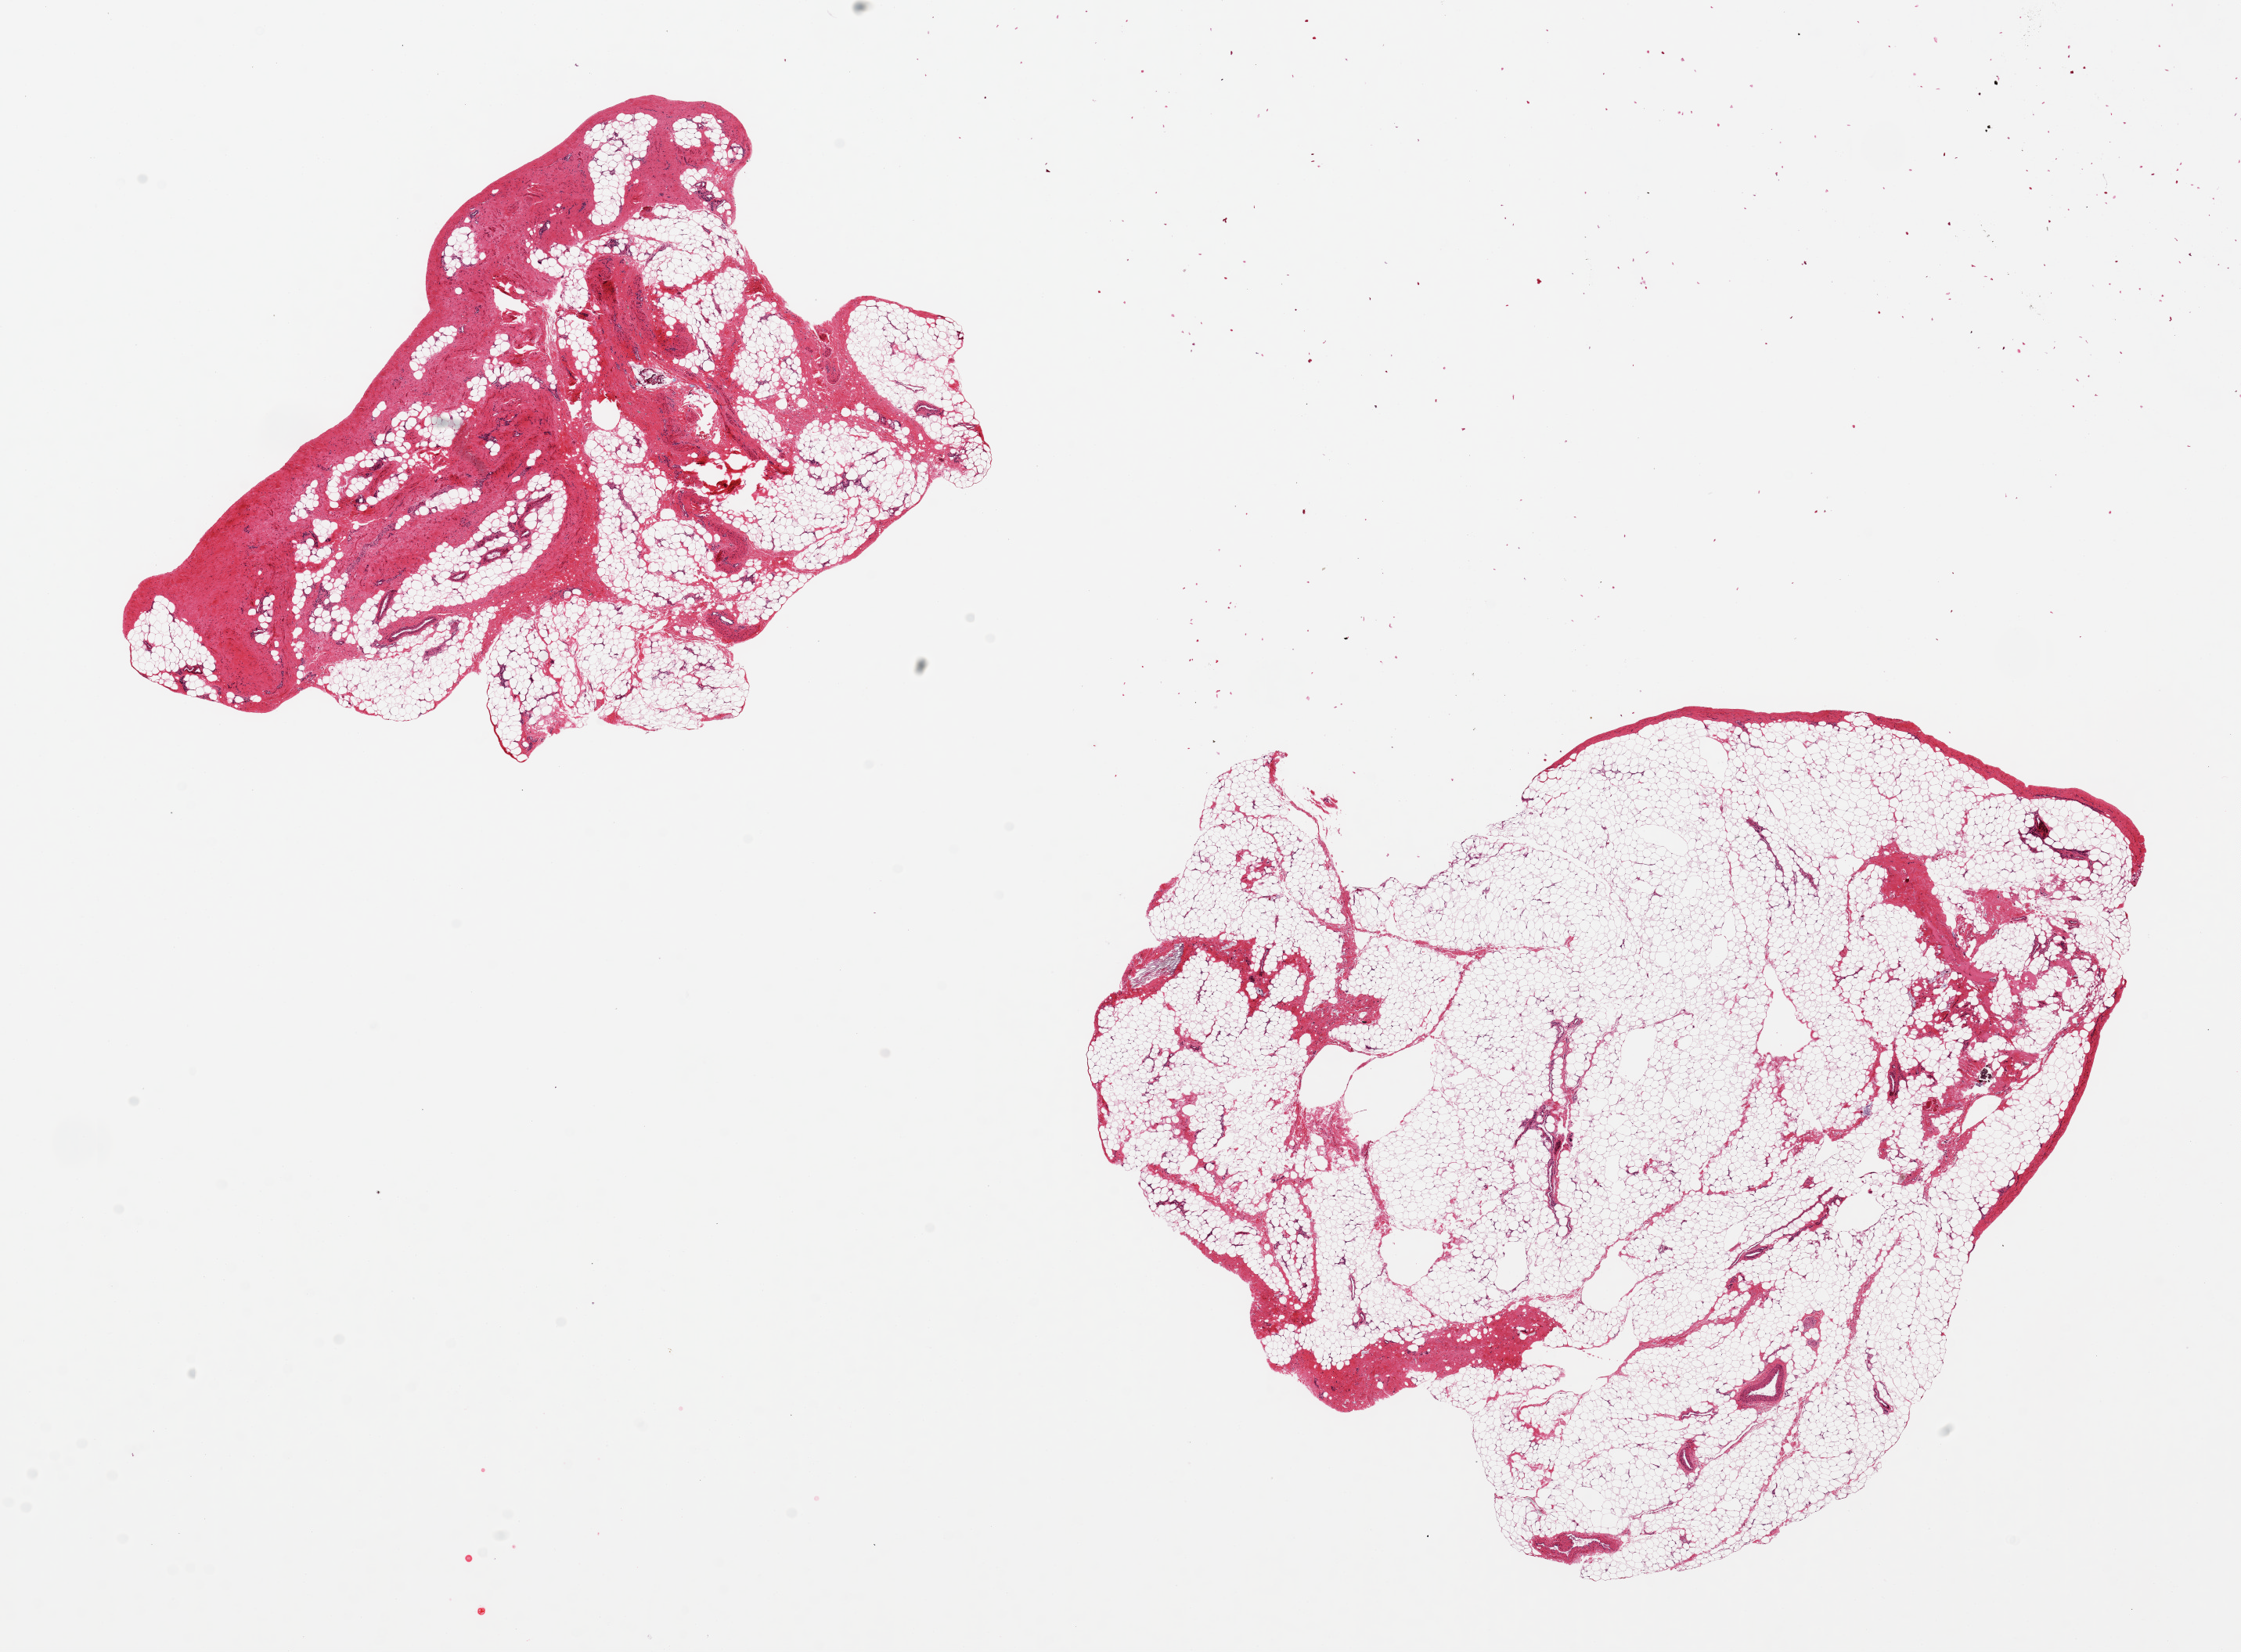
Haematoxylin and eosin whole-slide image, brightfield — low-resolution overview of the scanned area, about 22.6 x 16.7 mm (slide scanned at 20x). PAXgene-fixed paraffin-embedded (PFPE) section. Sampled site (target tissue): prostate. Tissue donor sample. Donor sex: male.
• review note (as recorded): 2 pieces, 8x5 & 10x9.5mm; no prostate, only fibroadipose tissue